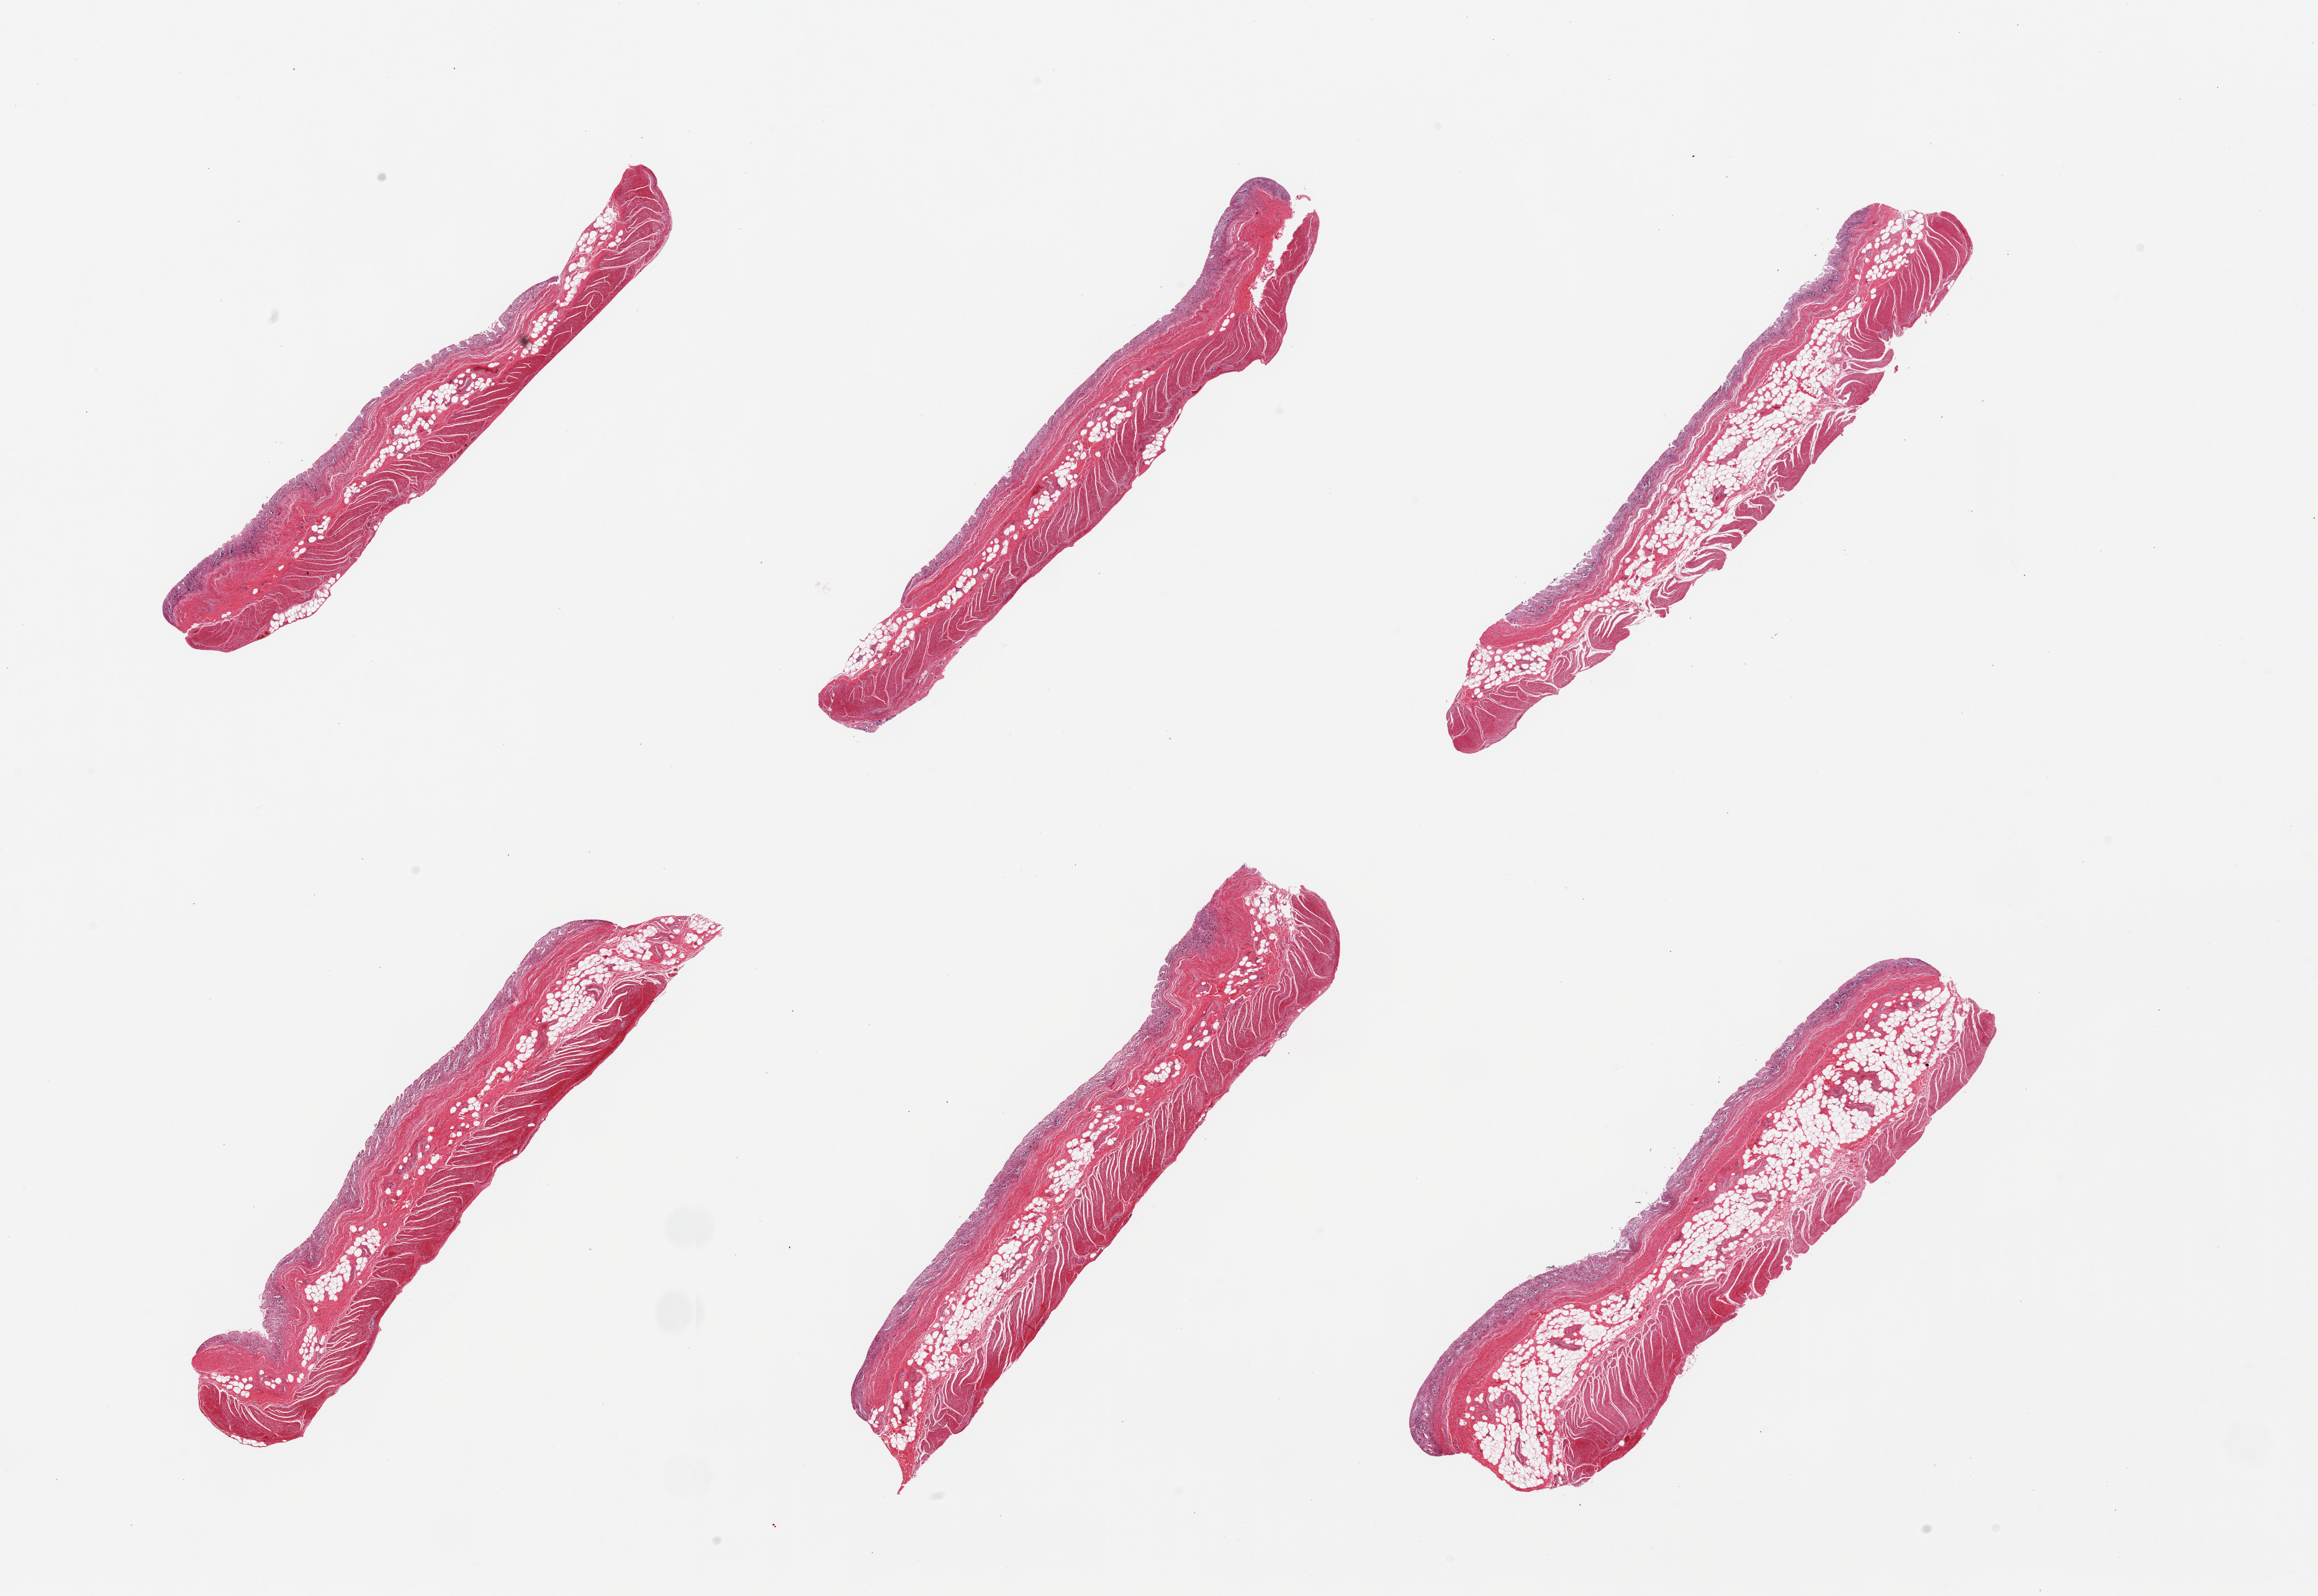
Whole-slide image, haematoxylin and eosin stain, a low-resolution overview of the entire scanned area, about 29.5 x 20.3 mm; PAXgene-fixed, paraffin-embedded tissue; target tissue: transverse colon; tissue donor sample. Donor: male.
Pathologist's review note for this sample: 6 pieces; full thickness with severe mucosal autolysis.